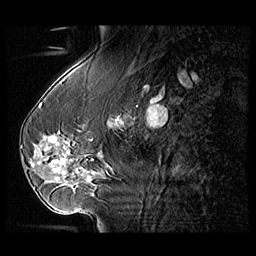
Breast MRI (dynamic contrast-enhanced), one sagittal slice; position 42 of 104 along the scan axis; 3 images stored at this slice position (order not interpretable as contrast timing); 1.5 T; TE 1.3 ms, TR 5.5 ms; 3 mm slice thickness; 256 × 256 image matrix. Patient: female, 54 years. From the clinical record (not read from this slice): setting: breast cancer imaged before/during neoadjuvant chemotherapy; receptor status: HR-positive, HER2-negative.
Outlined on this slice (semi-automatic segmentation, software-assisted and operator-edited):
- analysis volume of interest (the breast-tissue region the enhancement analysis was run in; not a lesion): bounding box [x1, y1, x2, y2] px = [28, 127, 104, 182]
- tumour enhancement mask (voxels above the 140 % enhancement threshold inside the analysis volume of interest): [49, 137, 66, 174]